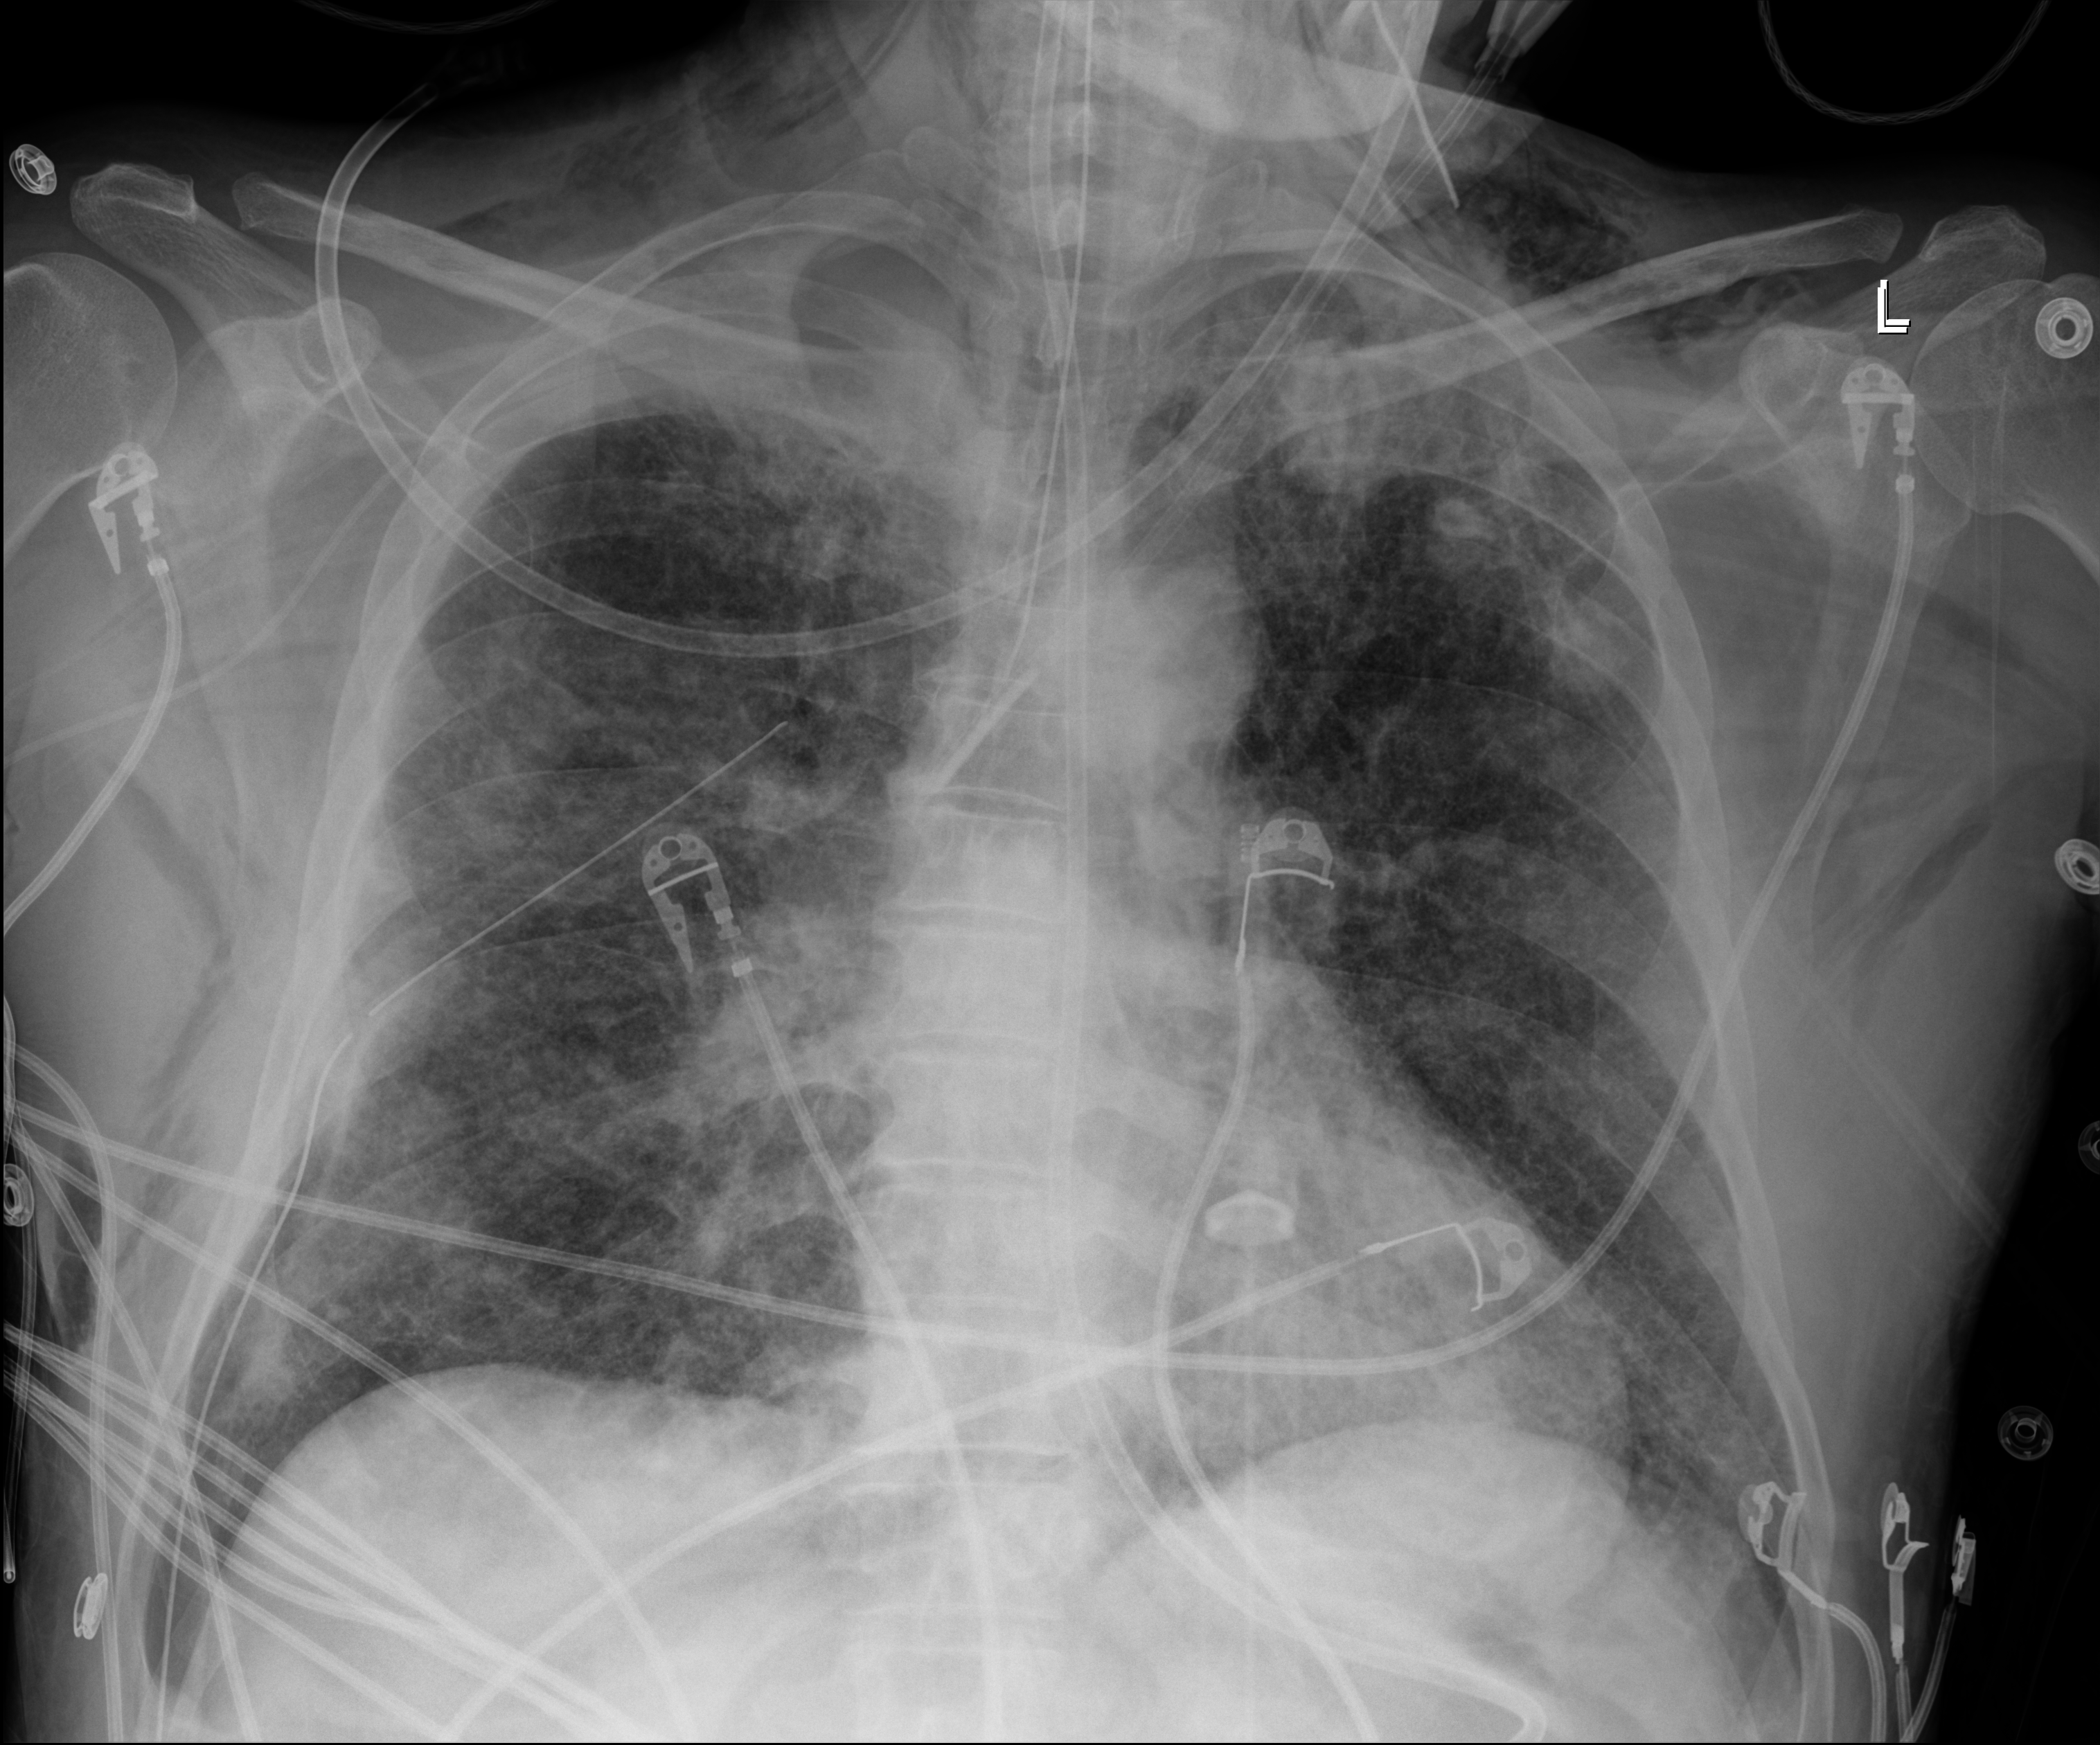
Bedside chest radiograph (digital radiography), anteroposterior (AP) projection. Patient hospitalised with COVID-19; male, aged 18–59 years.
From the hospital-stay record, not from the radiograph (when in the stay this image was taken is not recorded):
- diabetes (admission record): no
- smoking status (admission record): never
- mechanically ventilated during this hospital stay: yes